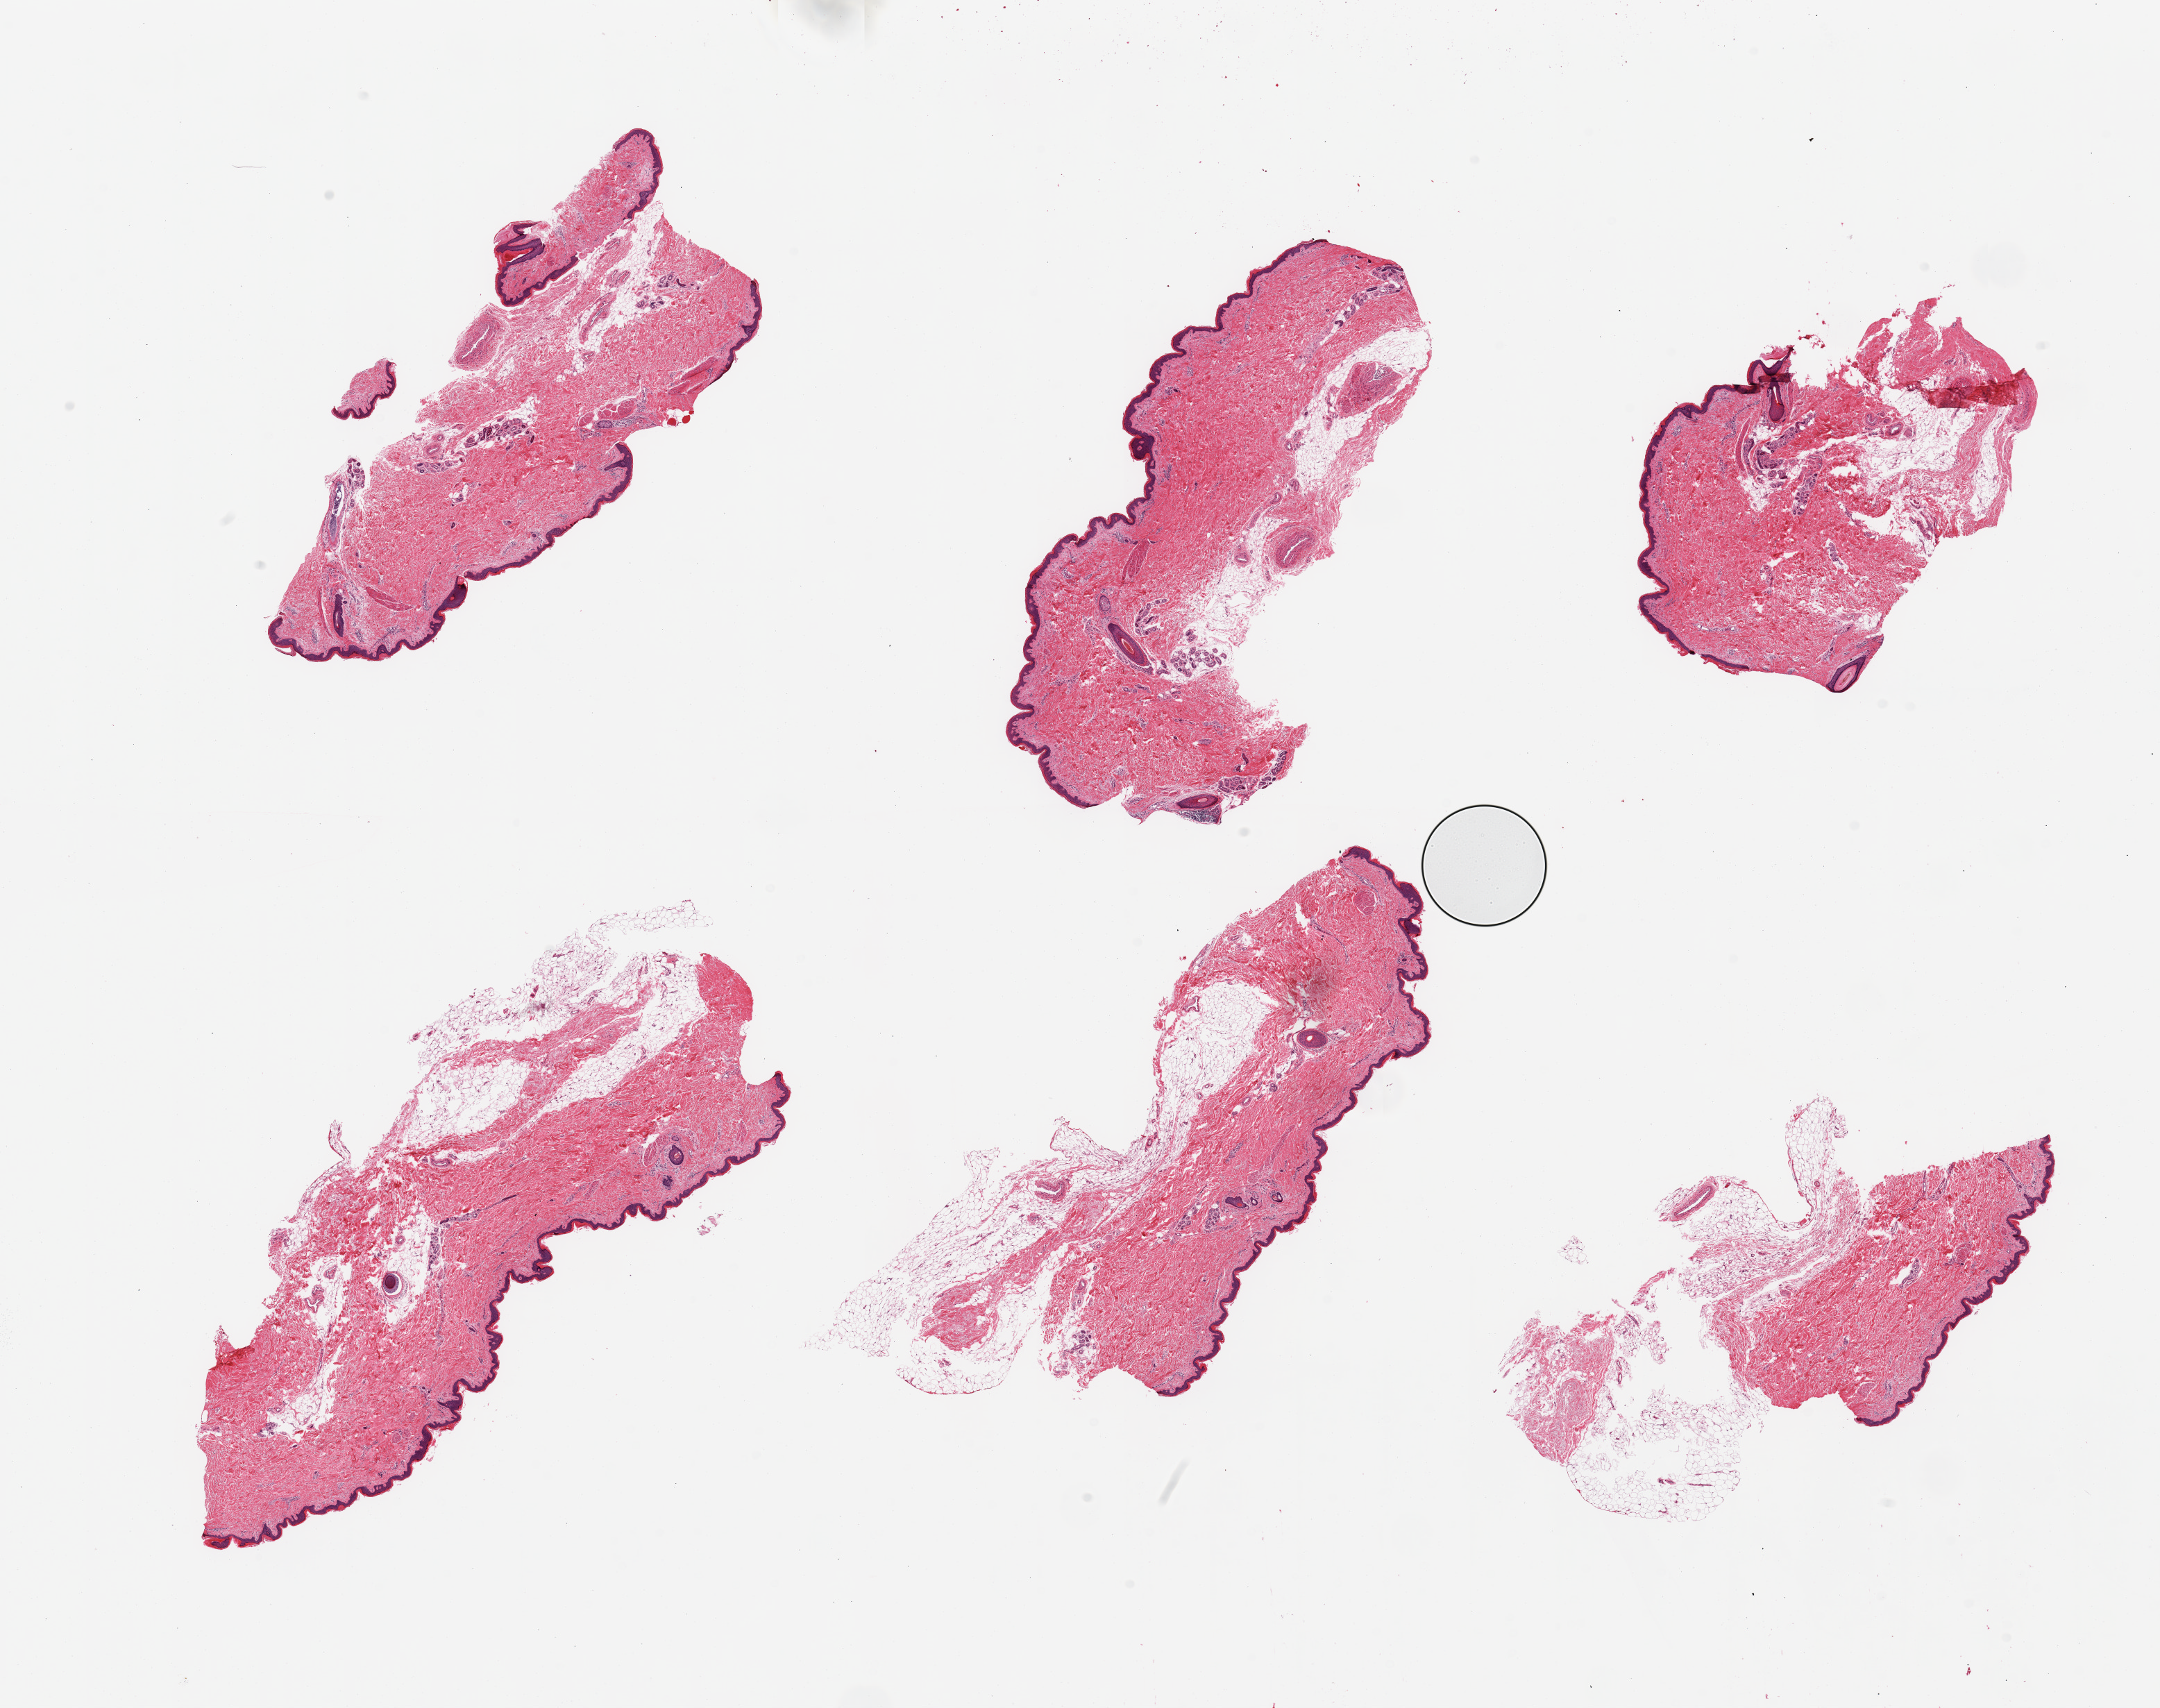
Digitized hematoxylin and eosin (H&E)-stained section, low-resolution overview of the scanned area, about 24.6 x 19.5 mm (slide scanned at 20x). PAXgene-fixed, paraffin-embedded tissue. Section of skin of lower leg (target tissue). Donor tissue sample. Male donor.
Review note (as recorded): 6 pieces, adherent dermal fat up to ~1mm; squamous epithelium is ~50 microns.